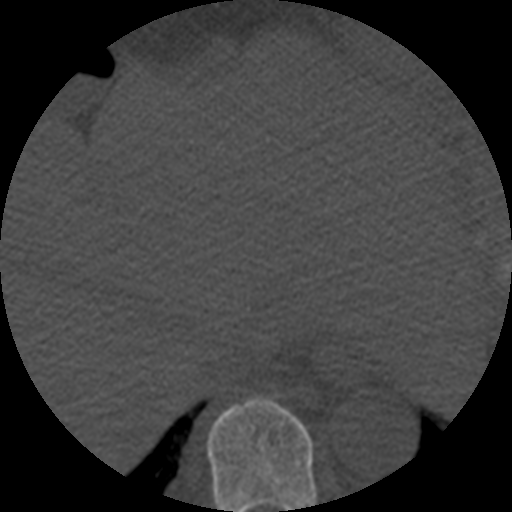
CT including the spine, one axial slice; slice 291 of 508 in the series (ordered by position); reconstruction kernel STANDARD; bone window (W 1800 / L 400 HU); 1.25 mm slice thickness; 512 × 512 image matrix, field of view 160 × 160 mm. Patient age 57 years. From the clinical record (not read from this slice): primary cancer: prostate.
Outlined on this slice (semi-automatic segmentation, software-assisted and operator-edited):
- T9 vertebra: box from (x=207, y=398) to (x=317, y=512) px